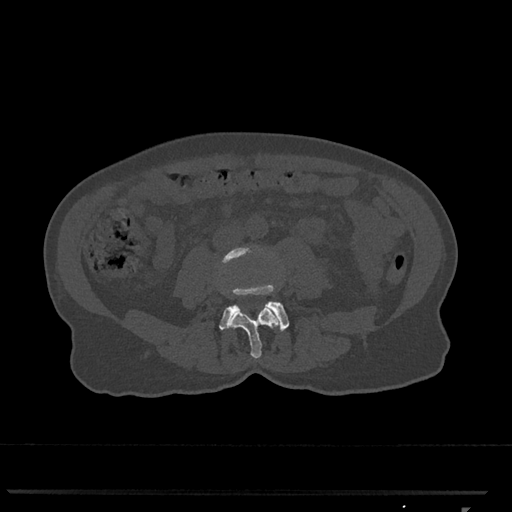
CT including the spine, one axial slice; reconstruction kernel Br40s/3; bone window (W 1800 / L 400 HU); 0.5 mm slice thickness; 512 × 512 image matrix, field of view 380 × 380 mm. Patient: female, 62 years. From the clinical record (not read from this slice): primary cancer: renal.
Structures marked on this image (semi-automatic segmentation, software-assisted and operator-edited):
- L3 vertebra: box from (x=222, y=247) to (x=280, y=359) px
- L4 vertebra: (x=219, y=285)–(x=289, y=332)